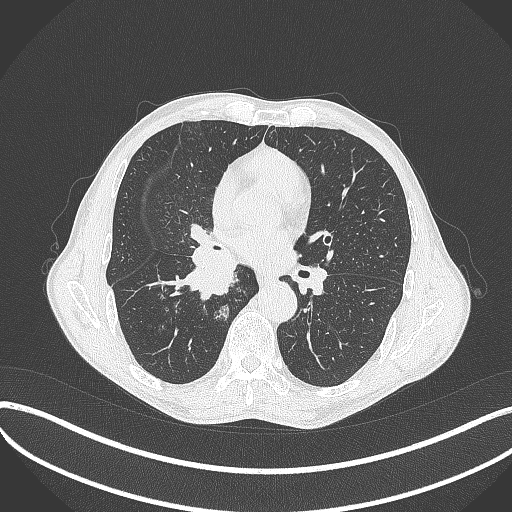
Chest CT, one axial slice; position 221 of 481 along the scan axis; reconstruction kernel B70f; 120 kVp; lung window (W 1500 / L -600 HU); 512 × 512 image matrix. Patient: male, 65 years. From the clinical record (not read from this slice): clinical TNM (as recorded): T2a N0 M0; histopathological grade: G2.
Annotated regions visible in this slice (bounding box drawn by a radiologist):
- lung tumour (recorded histology: squamous cell carcinoma): box from (x=178, y=246) to (x=246, y=301) px